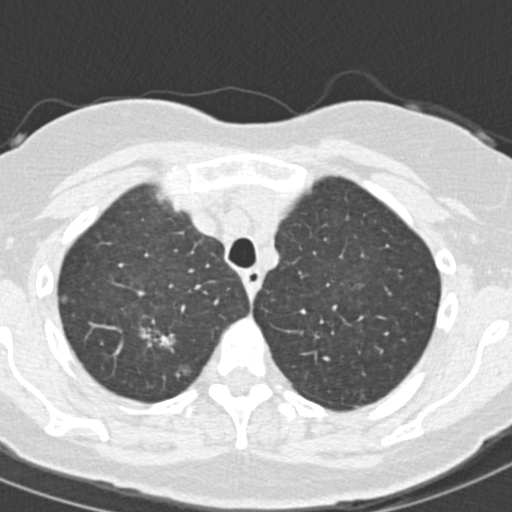
Low-dose screening chest CT, one axial slice. Position 124 of 157 along the scan axis. 120 kVp. Lung window (W 1500 / L -600 HU). 2 mm slice thickness. 512 × 512 image matrix, field of view 280 × 280 mm.
Structures marked on this image (expert manual segmentation):
- lesion 1 (tumor, upper lobe of right lung): bounding box (x1, y1, x2, y2) in pixels: (138, 313, 177, 353)